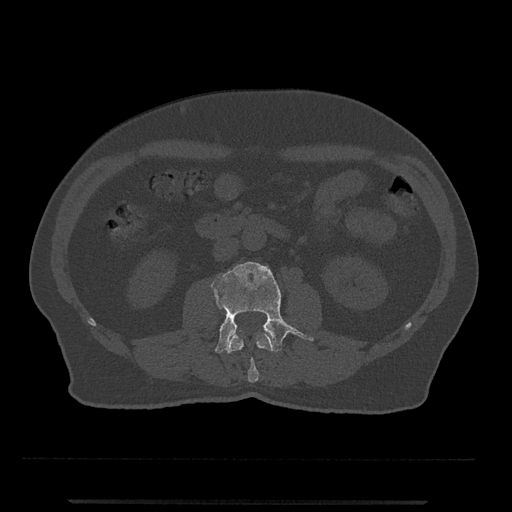
CT including the spine, one axial slice; position 223 of 797 along the scan axis; 120 kVp; bone window (W 1800 / L 400 HU); 512 × 512 image matrix, field of view 419 × 419 mm. Male patient, age 63 years. From the clinical record (not read from this slice): primary cancer: prostate.
Outlined on this slice (semi-automatic segmentation, software-assisted and operator-edited):
- L2 vertebra: box from (x=227, y=333) to (x=274, y=383) px
- L3 vertebra: (x=210, y=261)–(x=314, y=354)